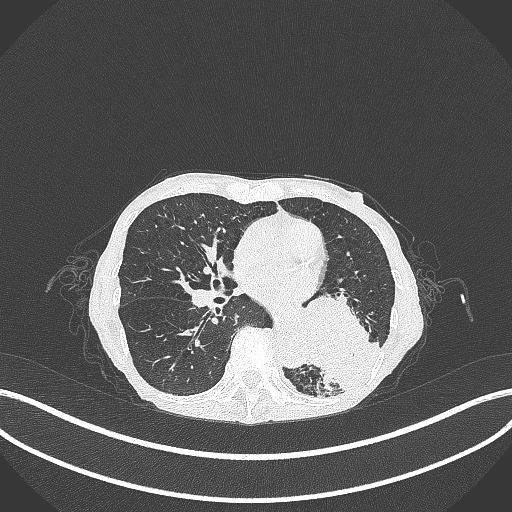
Chest CT, one axial slice; slice 127 of 347 in the series (ordered by position); lung window (W 1500 / L -600 HU); 1 mm slice thickness; 512 × 512 image matrix, field of view 400 × 400 mm. Female patient, age 70 years. Case-level facts recorded for this patient, not image findings: clinical TNM (as recorded): T3 N0 M0.
Annotated regions visible in this slice (bounding box drawn by a radiologist):
- lung tumour (recorded histology: small cell carcinoma): box from (x=301, y=292) to (x=387, y=394) px